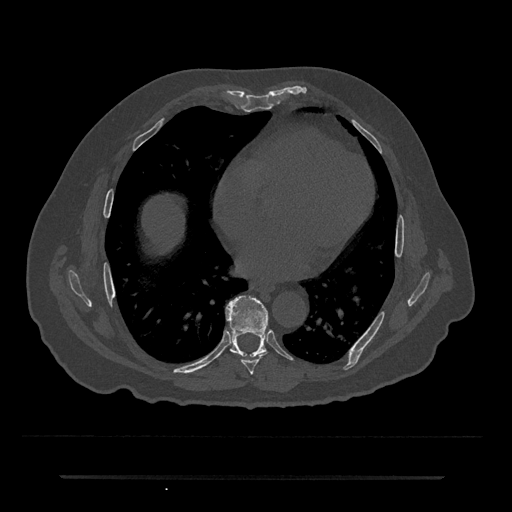
CT including the spine, one axial slice; position 359 of 797 along the scan axis; reconstruction kernel Br40s/3; bone window (W 1800 / L 400 HU); 512 × 512 image matrix. Patient: male, 69 years. Case-level facts recorded for this patient, not image findings: primary cancer: prostate.
Annotated regions visible in this slice (semi-automatically segmented with operator editing):
- T7 vertebra: bounding box <241,351,267,375> (left, top, right, bottom; pixels)
- T8 vertebra: <226,296,268,358>